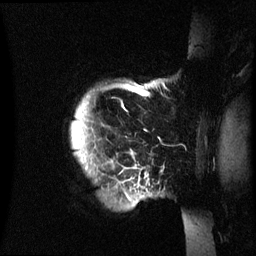
Breast MRI (dynamic contrast-enhanced), one sagittal slice. Slice 56 of 60 in the series (ordered by position). Dynamic contrast-enhanced series, image 2 of 3 at this slice position (ordered by acquisition). 1.5 T. TE 4.2 ms, TR 8.4 ms. 2.4 mm slice thickness. 256 × 256 image matrix, field of view 230 × 230 mm. Patient: female, 48 years.
Annotated regions visible in this slice (semi-automatic segmentation, software-assisted and operator-edited):
- analysis volume of interest (the breast-tissue region the enhancement analysis was run in; not a lesion): bounding box [x1, y1, x2, y2] px = [71, 82, 194, 234]
- tumour enhancement mask (voxels above the 70 % enhancement threshold inside the analysis volume of interest): [74, 84, 151, 200]